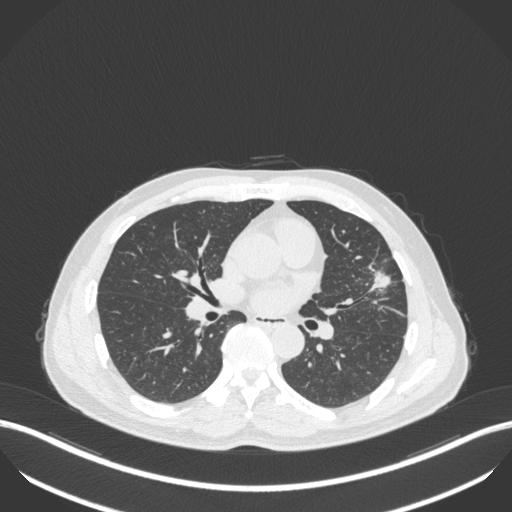
Chest CT, one axial slice; reconstruction kernel B31f; 120 kVp; lung window (W 1500 / L -600 HU); 1 mm slice thickness; 512 × 512 image matrix, field of view 400 × 400 mm. Male patient, age 55 years. From the clinical record (not read from this slice): clinical TNM (as recorded): T1c N0 M0; histopathological grade: G2-3.
Outlined on this slice (rectangle marked by the reading radiologist):
- lung tumour (recorded histology: adenocarcinoma): bounding box <365,264,395,294> (left, top, right, bottom; pixels)